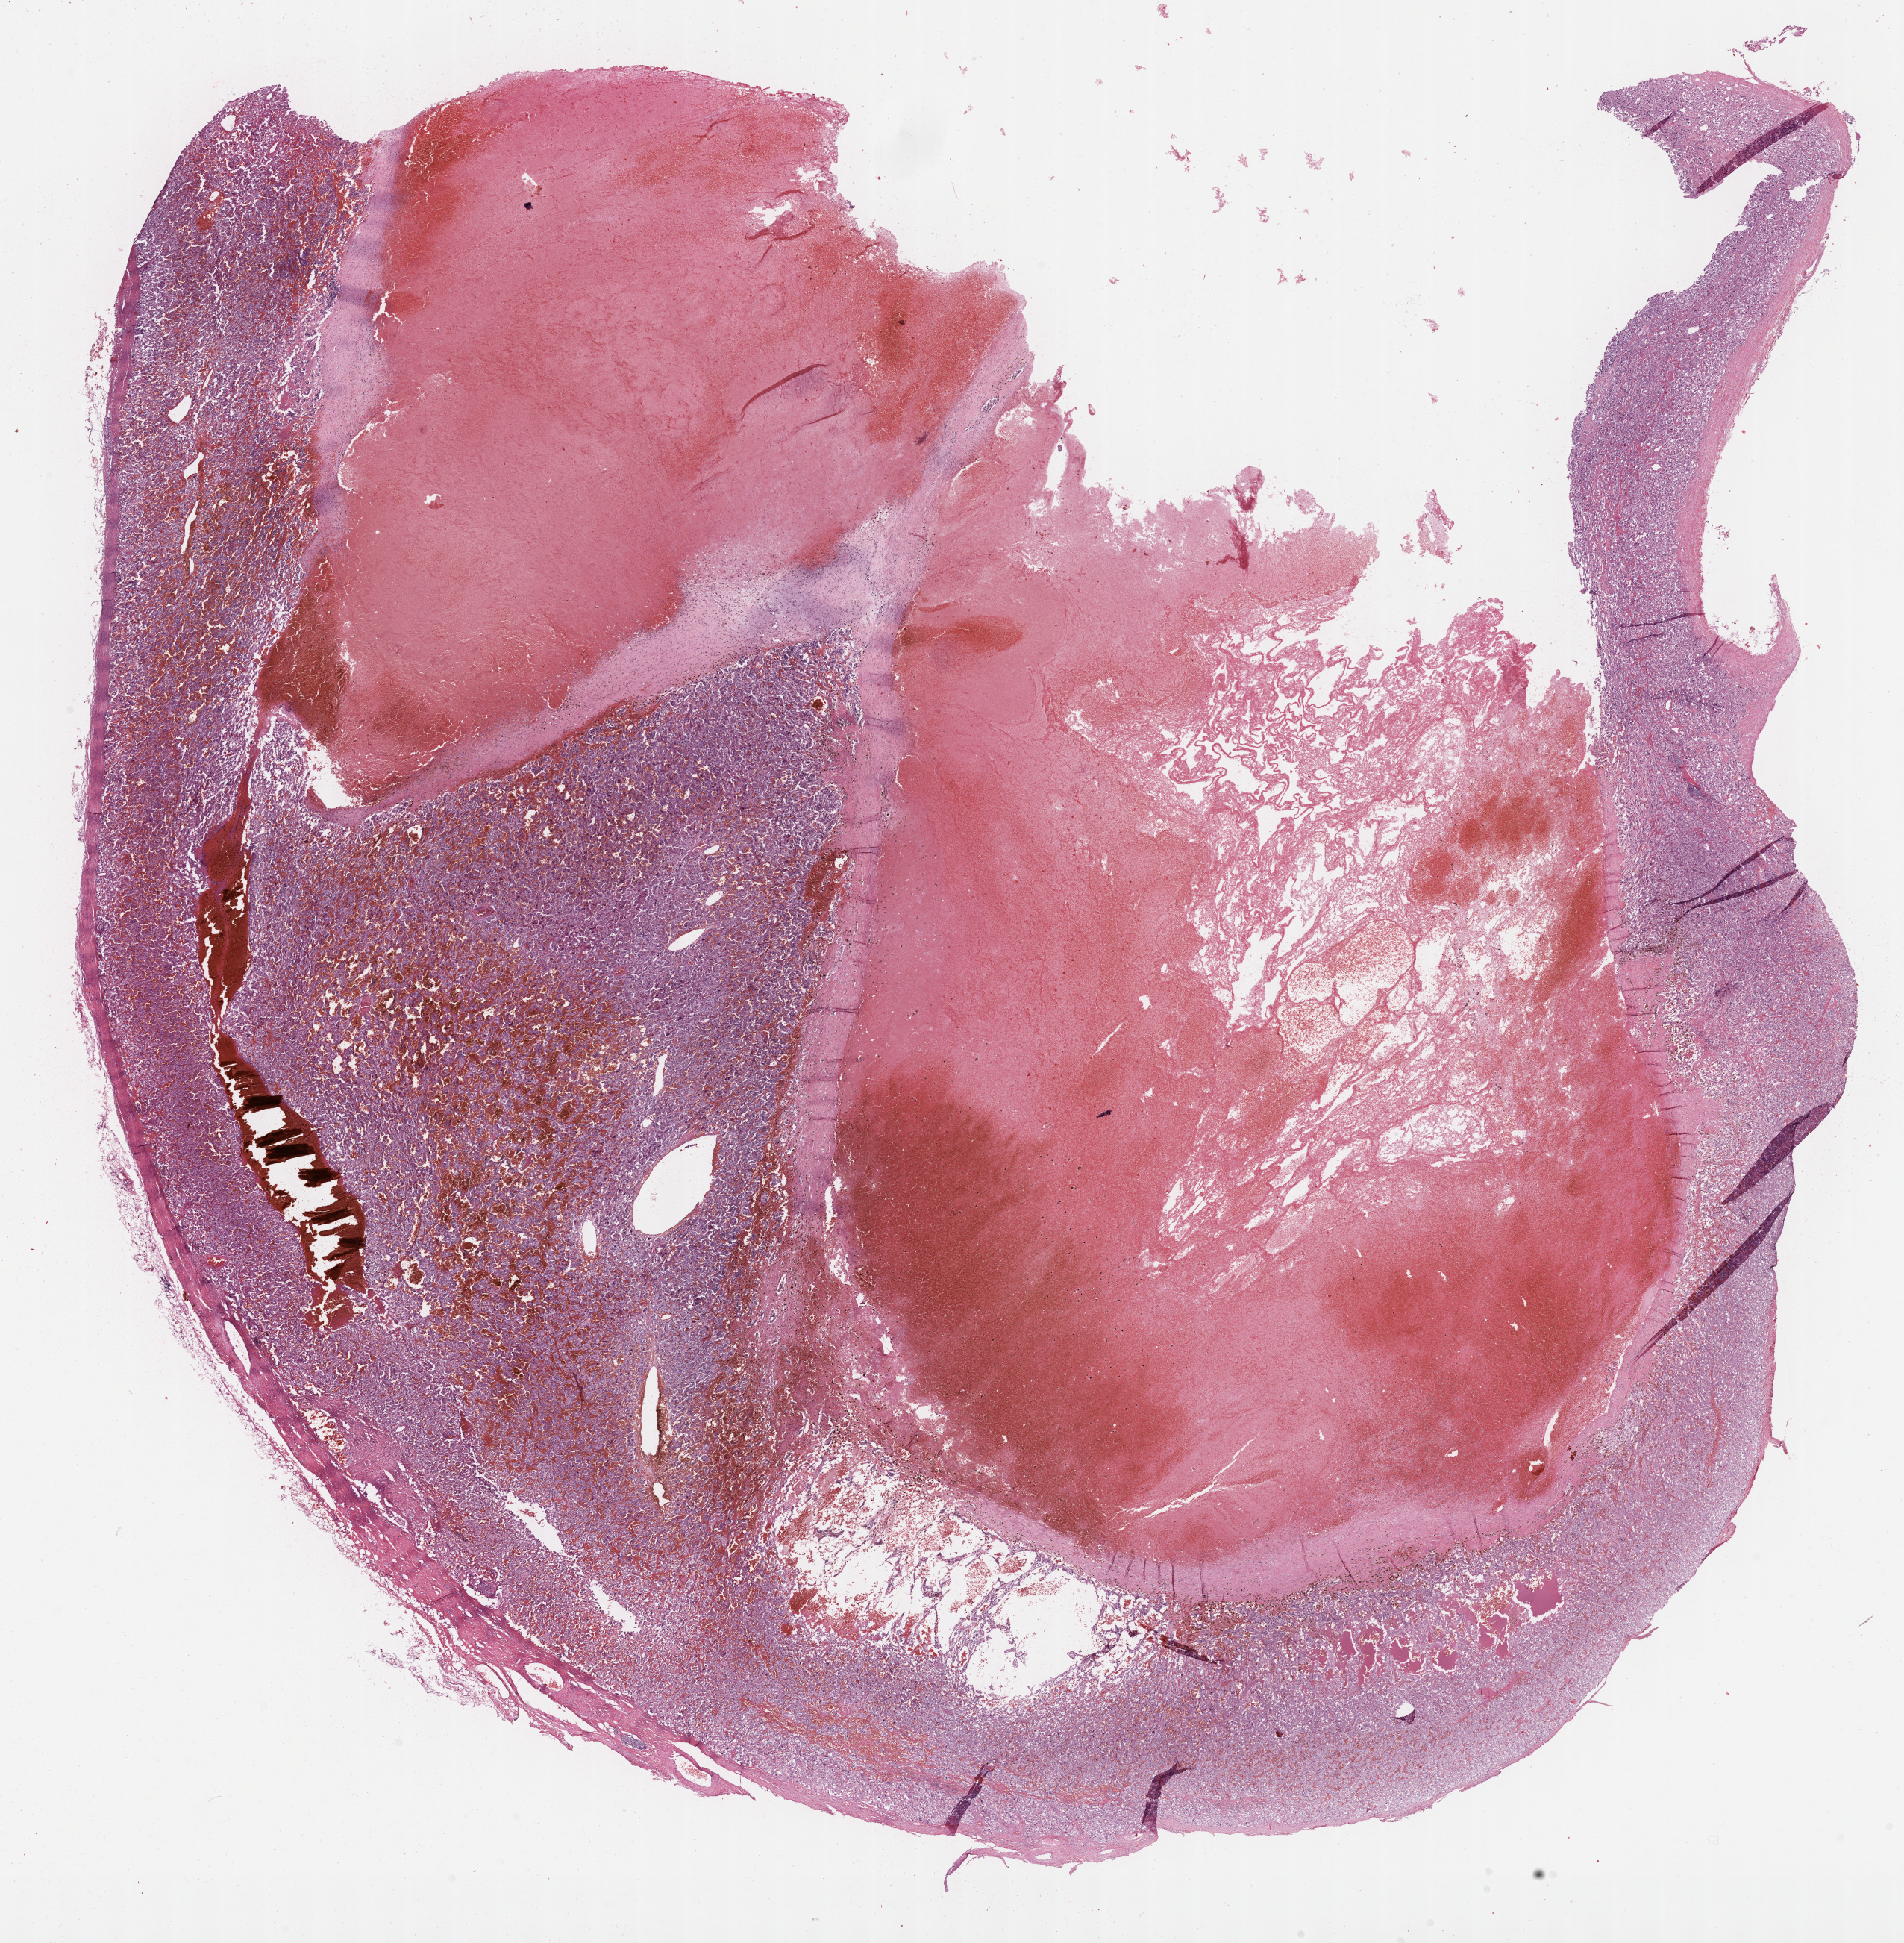
H&E whole-slide image, a low-resolution overview of the entire scanned area, about 20.6 x 21.1 mm; formalin-fixed paraffin-embedded (FFPE) diagnostic section; sample: primary tumour, adrenal gland. Patient: female, age at initial diagnosis 76 years.
Diagnosis: Pheochromocytoma, NOS.